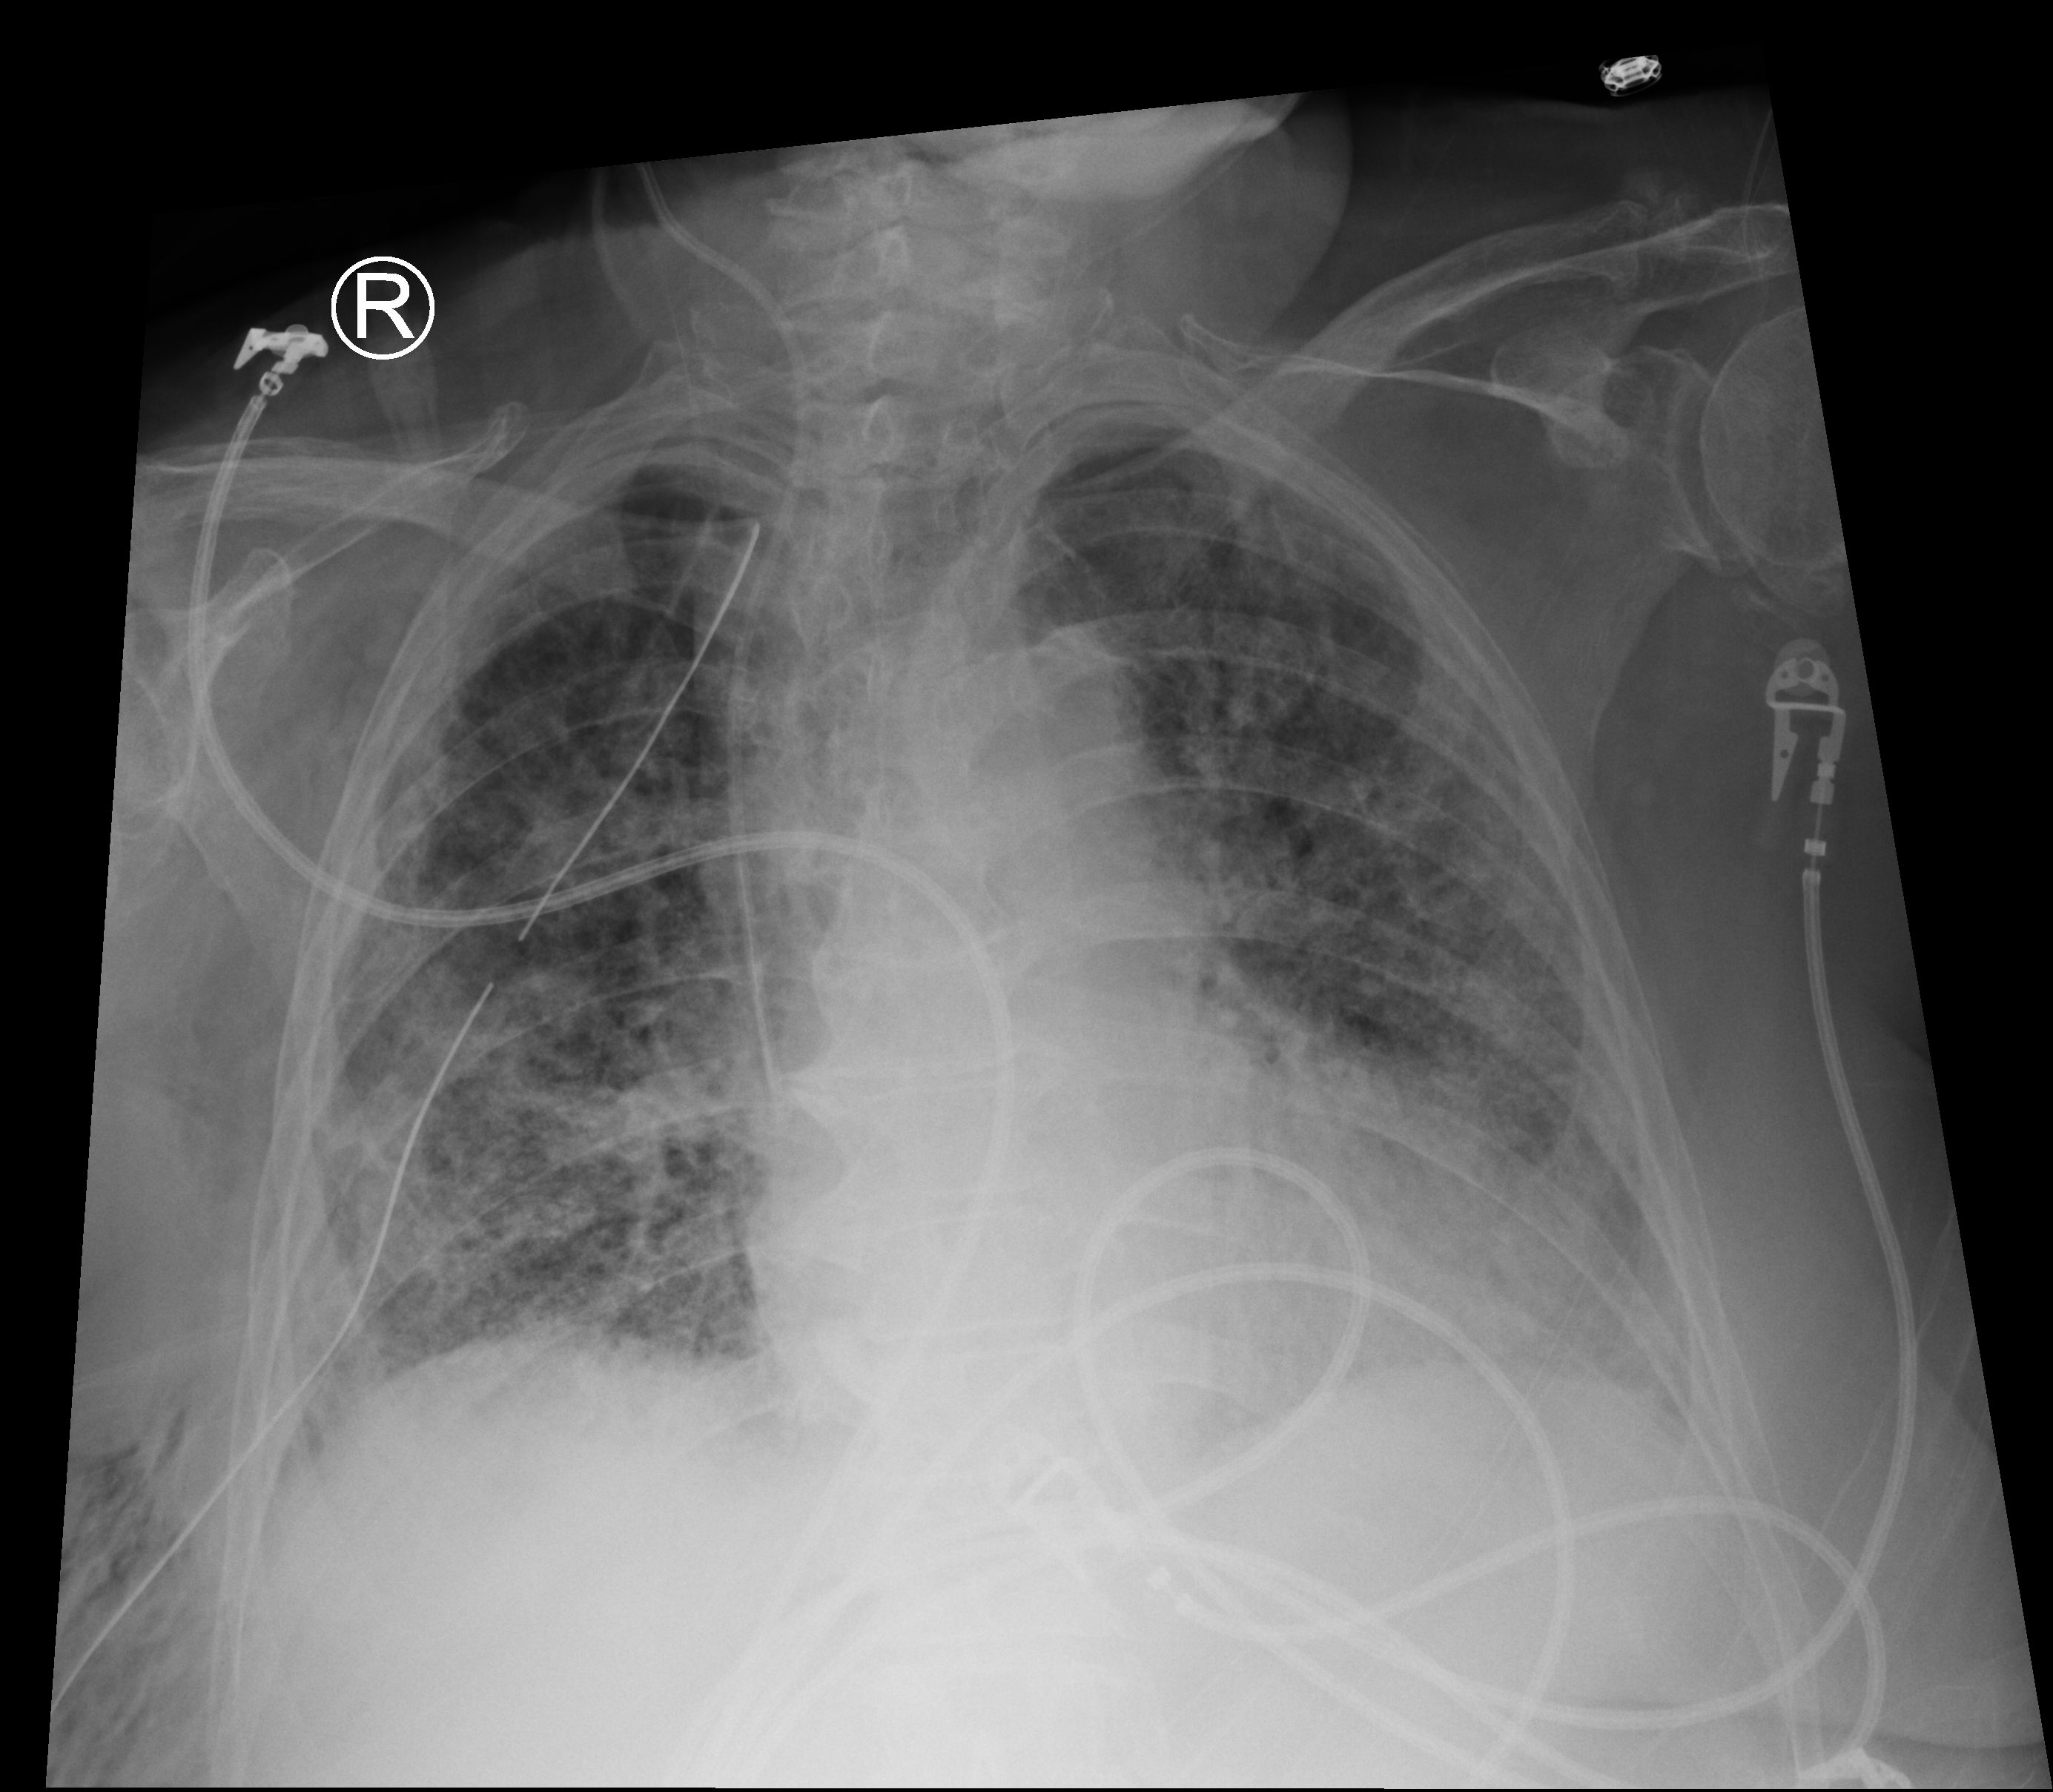
Bedside chest radiograph (computed radiography); anteroposterior (AP) projection. Patient hospitalised with COVID-19; female, aged 75–90 years.
Hospital-stay facts (about this admission, not read from this image; timing relative to this image not recorded): admitted to intensive care during this hospital stay: no; mechanically ventilated during this hospital stay: yes; length of hospital stay: 56 days.